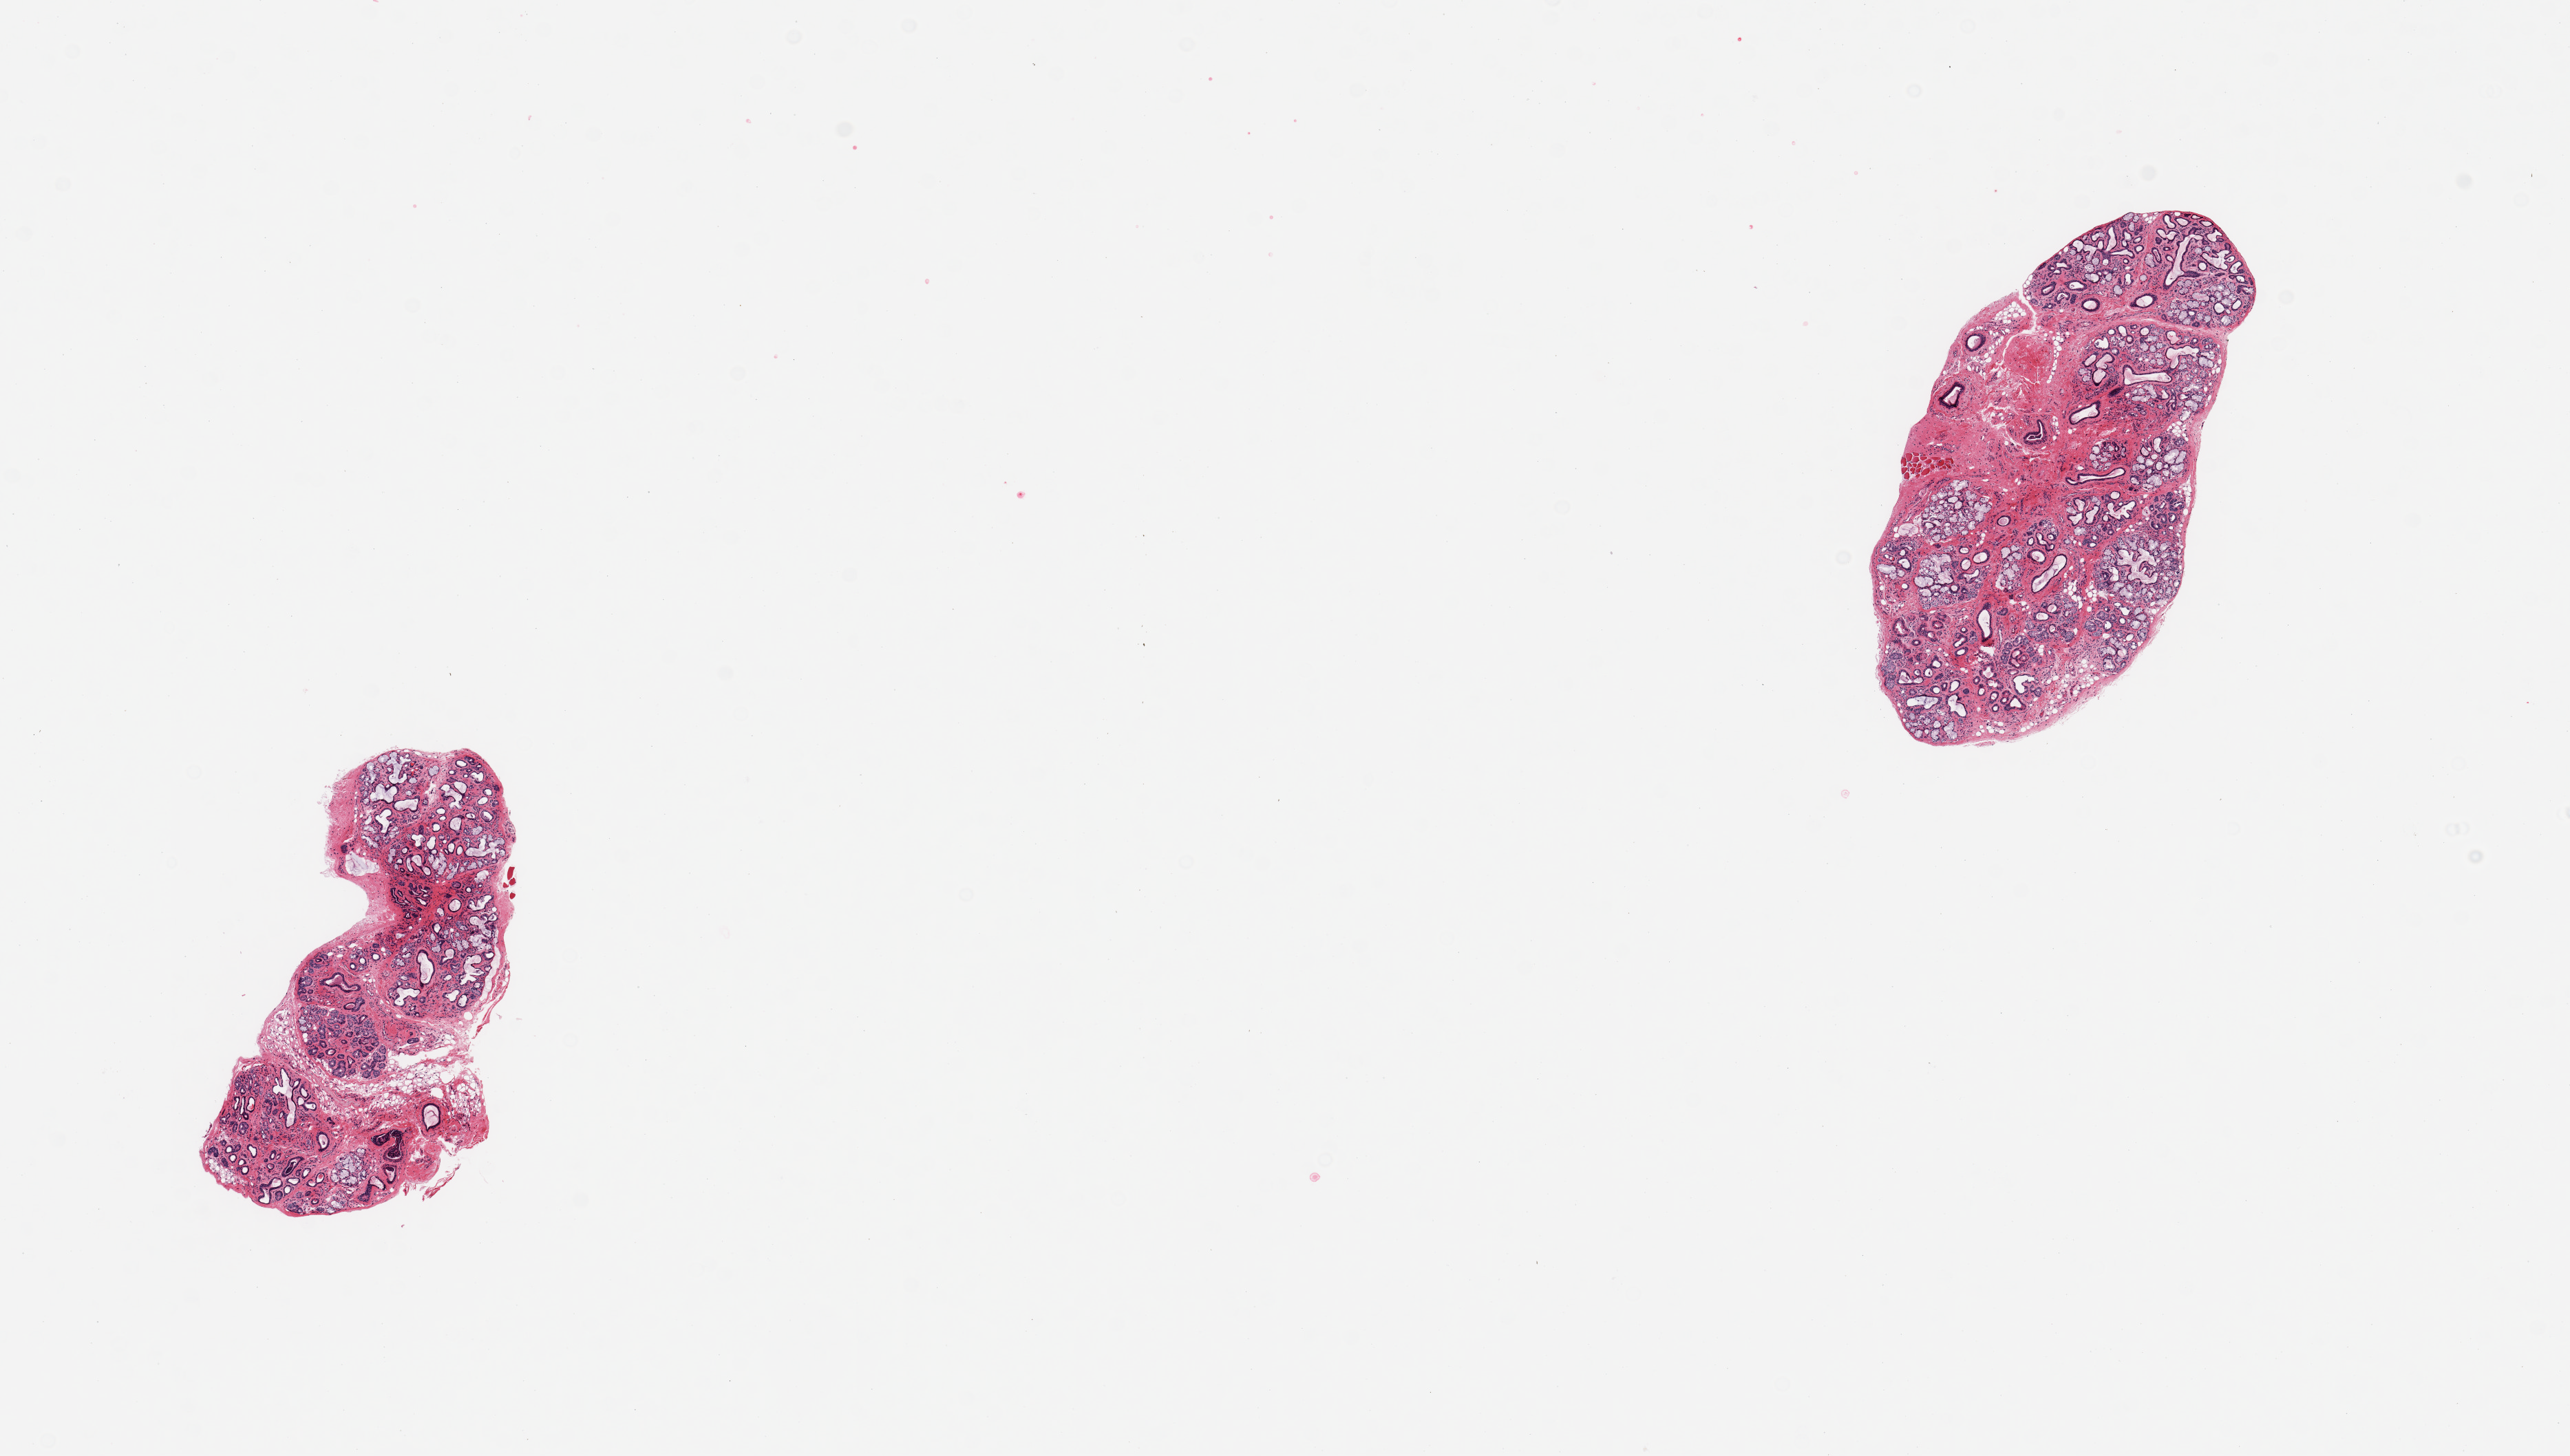
Digitized H&E-stained section, brightfield, a low-resolution overview of the entire scanned area, about 14.8 x 8.4 mm (from a 20x scan); PAXgene-fixed paraffin-embedded (PFPE) section; section of minor salivary gland (target tissue); tissue donor sample. Donor sex: male.
- reviewer comment on this tissue sample: 2 pieces; moderately to severely atrophic, fibrotic glands with ductal dilatation